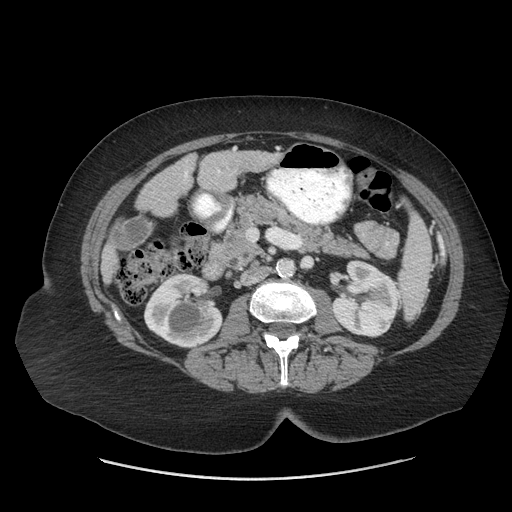
Contrast-enhanced abdominal CT (liver protocol), one axial slice. Slice 18 of 69 in the series (ordered by position). 140 kVp. Soft-tissue window (W 400 / L 40 HU). 512 × 512 image matrix, field of view 420 × 420 mm. Case-level facts recorded for this patient, not image findings: diagnosis: hepatocellular carcinoma (patient treated with transarterial chemoembolisation; whether this scan precedes or follows treatment is not stated here); TNM stage (as recorded): Stage-IIIB; Child-Pugh class: A; tumour differentiation: moderately differentiated; tumour nodularity: multinodular.
Structures marked on this image (semi-automatic segmentation, software-assisted and operator-edited):
- liver parenchyma outside the tumour (the mass and vessels are separate outlines, so this box may not span the whole liver): box from (x=100, y=148) to (x=280, y=283) px
- liver vessels: (x=218, y=170)–(x=220, y=172)